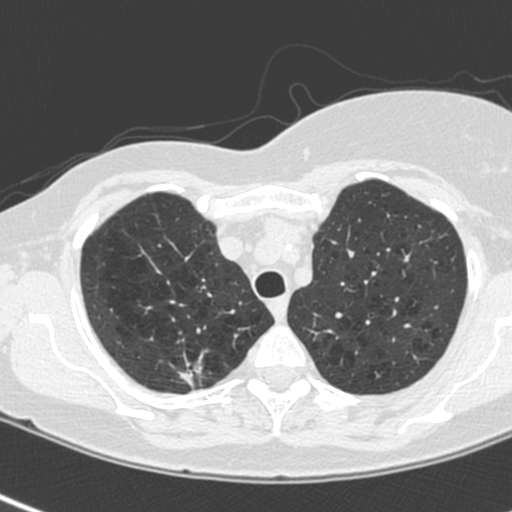
Low-dose screening chest CT, axial slice; baseline screening round; lung window (W 1500 / L -600 HU); 1.3 mm slice thickness; standard (soft-tissue) reconstruction kernel (C); 512 × 512 image matrix. Female, age 64 years at enrolment.
Expert-annotated lung lesion, bounding box [x1, y1, x2, y2] px = [167, 351, 222, 403]. The exam's reader record, not a measurement of the box and not confirmed to be the same lesion: non-calcified nodule or mass ≥4 mm, right upper lobe, 13 × 10 mm, spiculated (stellate) margins, soft tissue attenuation. Official screen result: positive, change unspecified: nodule(s) >= 4 mm or enlarging nodule(s), mass(es), or other non-specific abnormalities suspicious for lung cancer. Later outcome: lung cancer diagnosed 21 days after this screen — adenocarcinoma, NOS, right upper lobe, poorly differentiated (G3), stage IIIB (AJCC 6th edition), 20 mm at pathology.